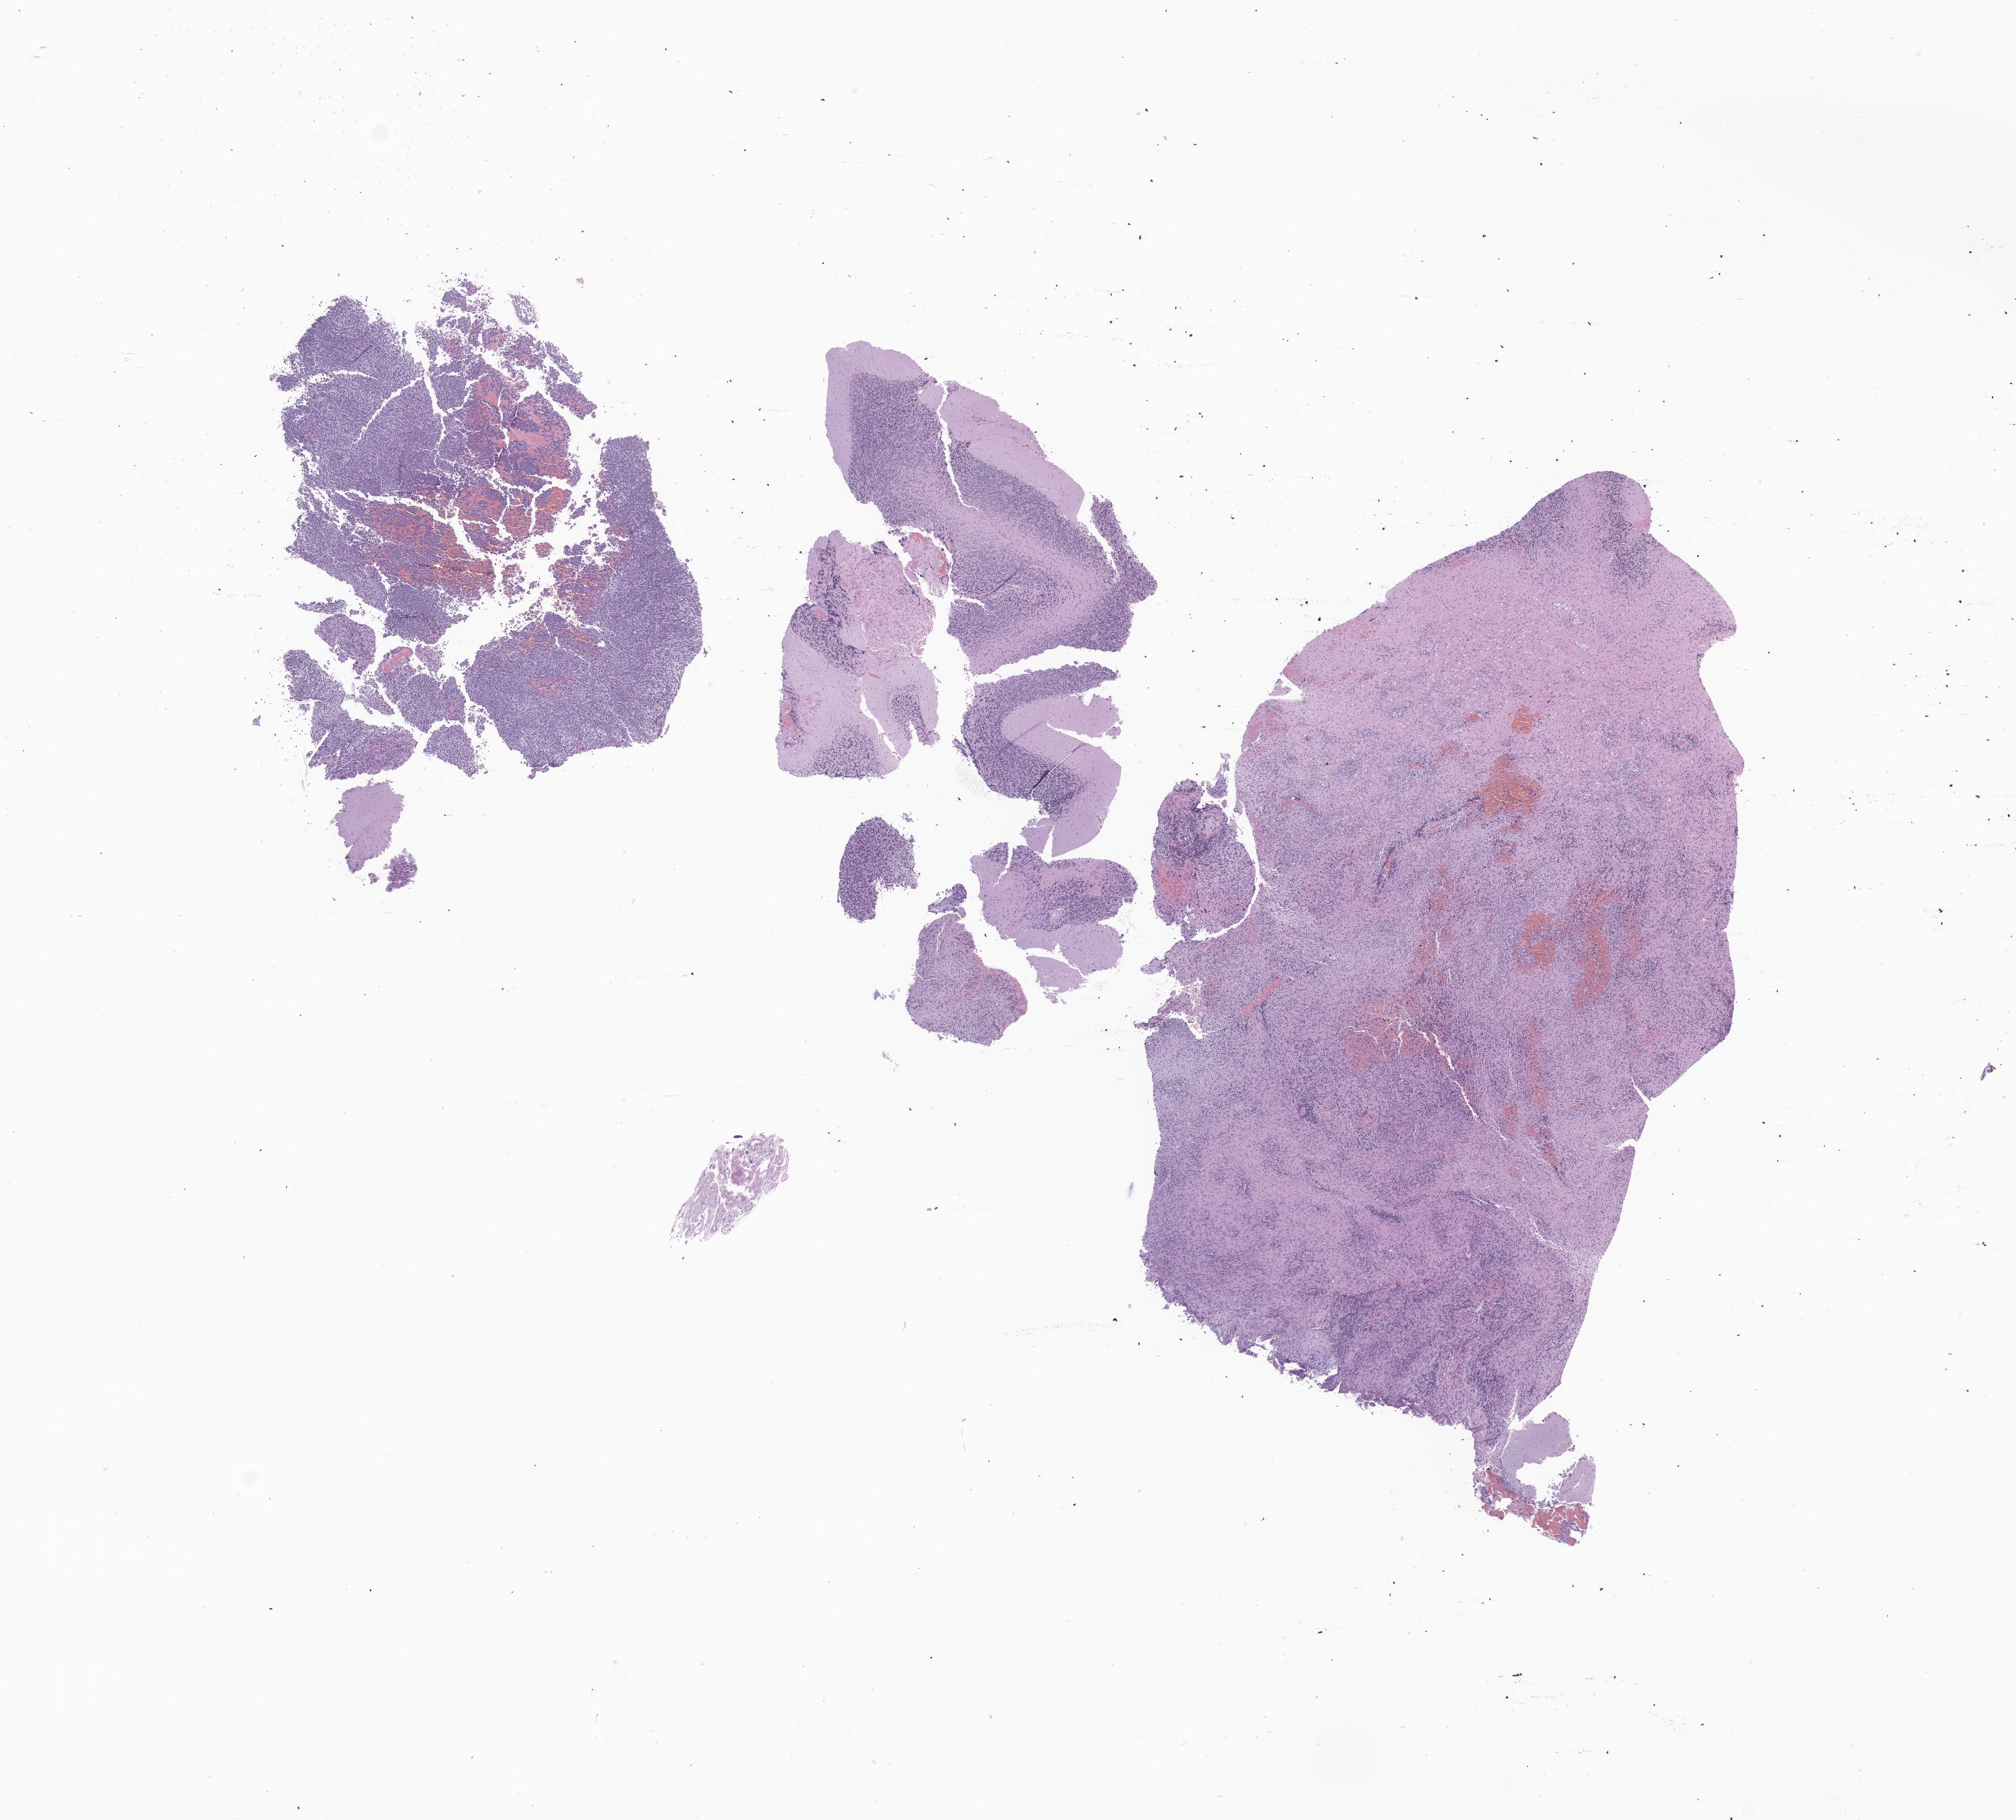
Whole-slide image, H&E stain of tumor tissue from the brain — low-resolution overview of the scanned area, about 13.7 x 12.4 mm. Formalin-fixed paraffin-embedded section. Male patient, age 225 months (18 years 9 months).
Diagnosis: Medulloblastoma, NOS.